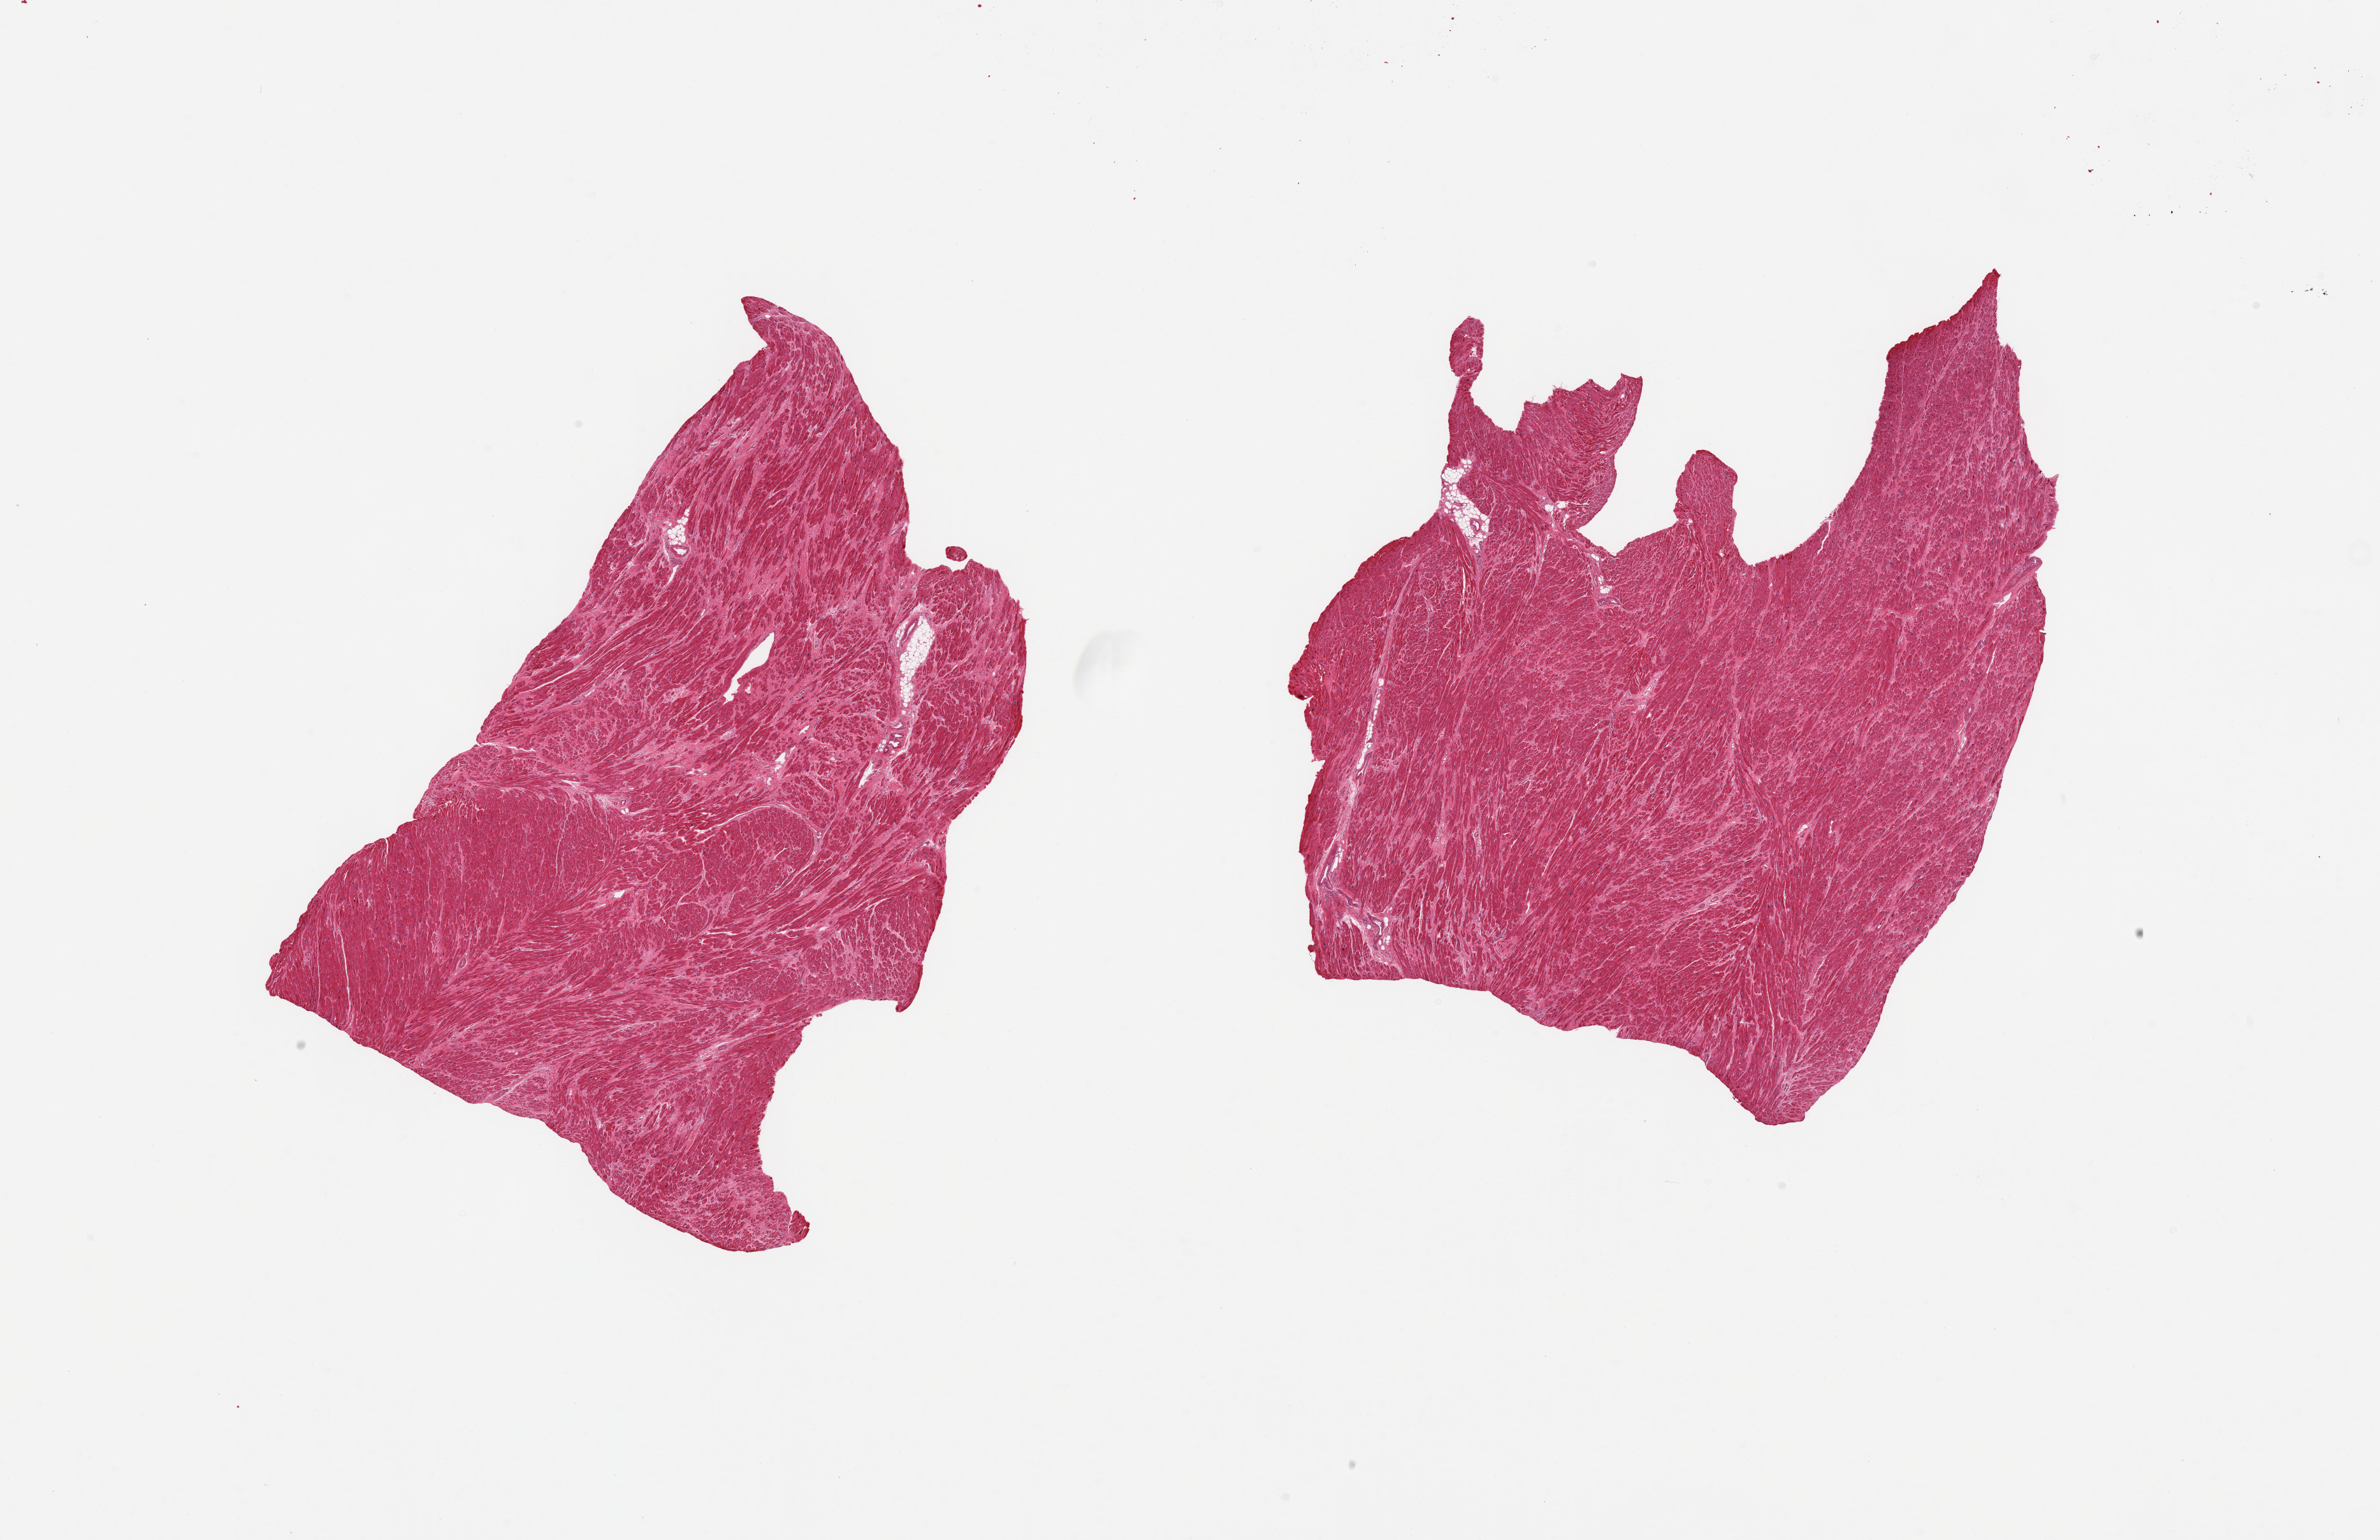
H&E whole-slide image, shown as a low-resolution overview of the whole scanned area (about 29.5 x 19.1 mm, acquisition: 20x scan), PAXgene-fixed paraffin-embedded (PFPE) section, section of heart (target tissue), donor tissue sample. Female donor.
Review note (as recorded): 2 pieces; interstitial and patchy fibrosis c/w prior ischemia, hypertrophy.